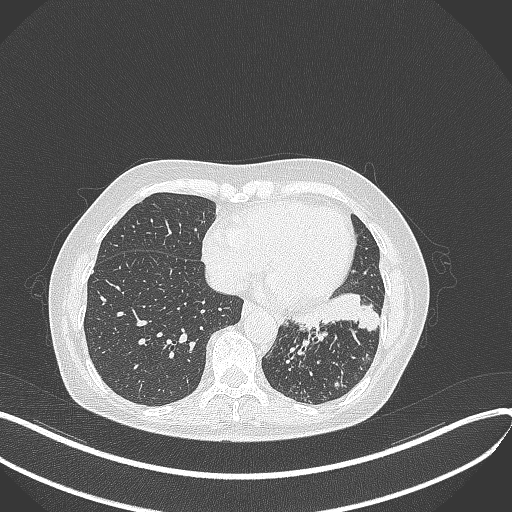
Chest CT, one axial slice; position 135 of 429 along the scan axis; reconstruction kernel B70f; 100 kVp; lung window (W 1500 / L -600 HU); 1 mm slice thickness; 512 × 512 image matrix. Patient: female, 63 years. From the clinical record (not read from this slice): clinical TNM (as recorded): T1b N0 M0; histopathological grade: G2-3.
Structures marked on this image (bounding box drawn by a radiologist):
- lung tumour (recorded histology: adenocarcinoma): bounding box (x1, y1, x2, y2) in pixels: (294, 293, 381, 337)